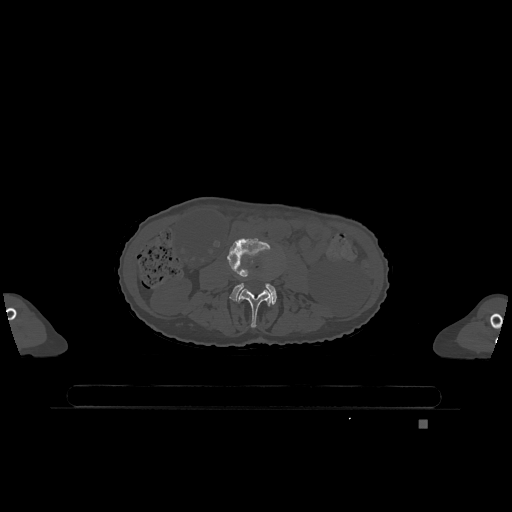
CT including the spine, one axial slice; slice 334 of 1317 in the series (ordered by position); bone window (W 1800 / L 400 HU); 512 × 512 image matrix. Patient: female, 74 years. Case-level facts recorded for this patient, not image findings: primary cancer: lung; vertebrae with lytic lesions (as recorded): T1, T4, T5, T6, L4, L5.
Structures marked on this image (semi-automatically segmented with operator editing):
- L3 vertebra: bounding box [x1, y1, x2, y2] px = [238, 289, 274, 328]
- L4 vertebra: [227, 239, 277, 304]